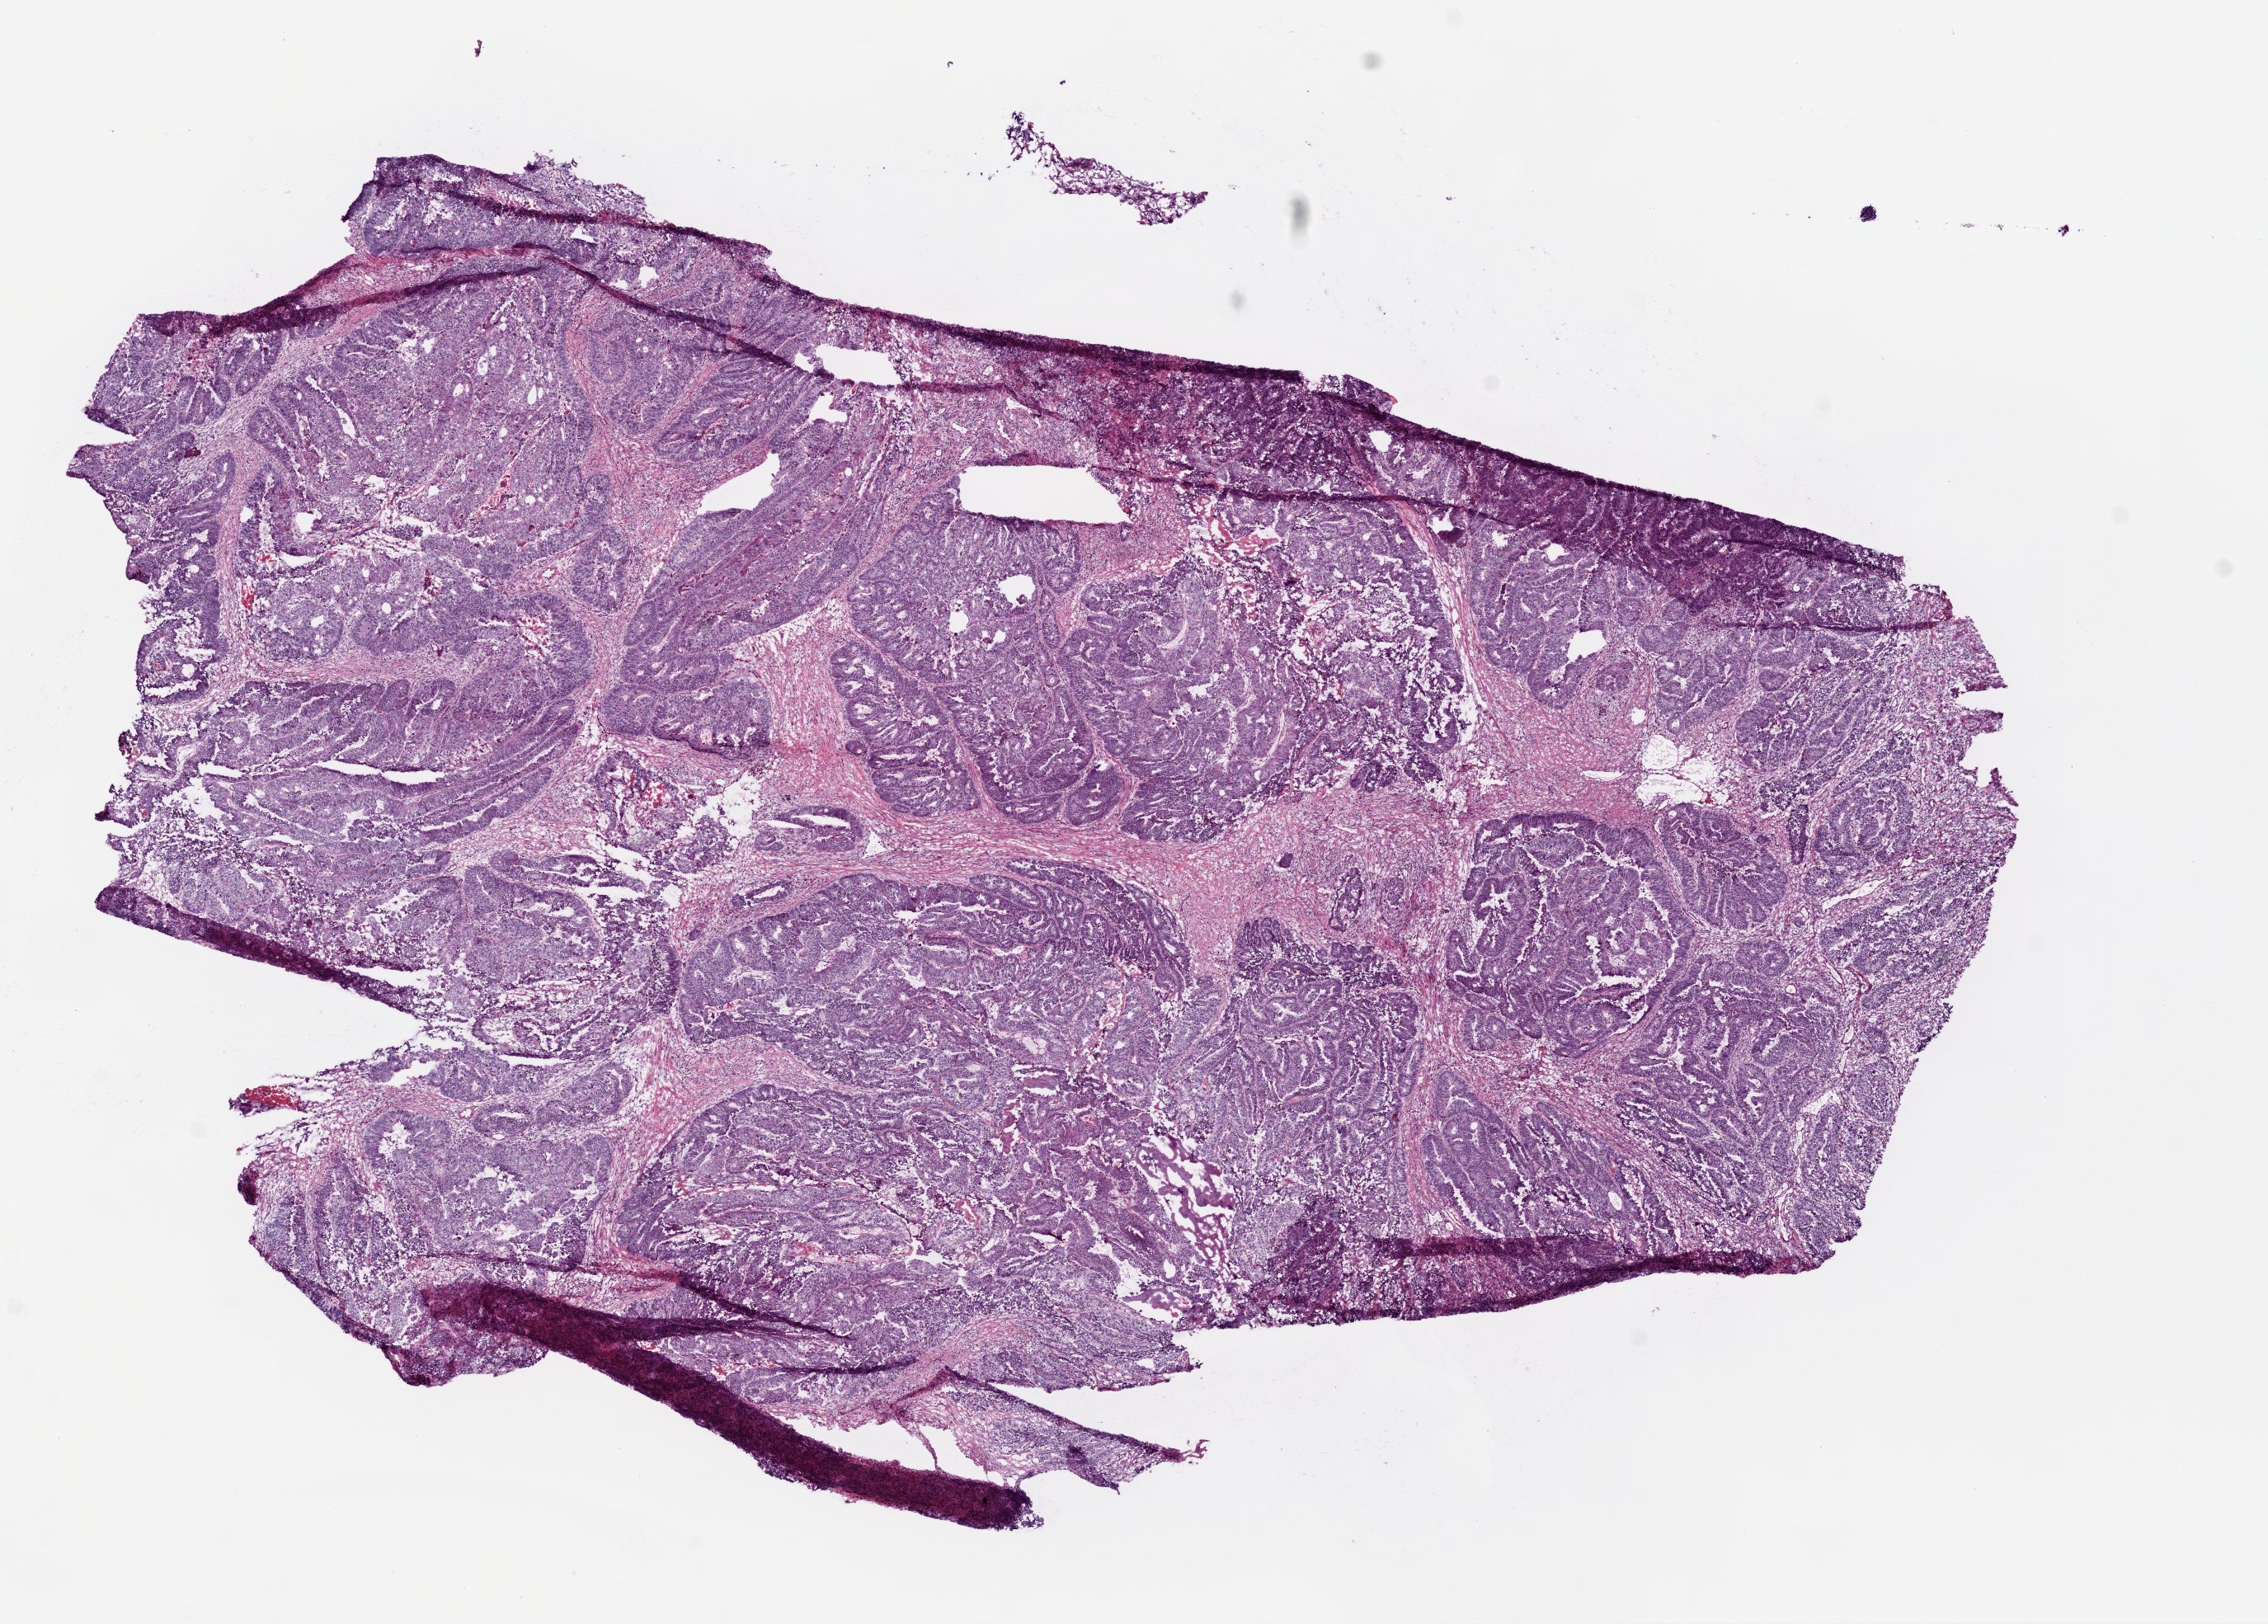
Digitized H&E tissue section (whole slide), a low-resolution overview of the entire scanned area, about 11.0 x 7.9 mm (acquisition: 20x scan). Frozen section. Sample: primary tumour, rectum. Female patient; age at initial diagnosis 85 years. Pathologist review of this section (percent, as recorded): tumour cells 75%, tumour nuclei 70%, normal cells 0%, stromal cells 15%, necrosis 10%.
Lymph nodes positive (case pathology): 0 of 18 examined. AJCC pathologic stage: I (5th edition). Diagnosis: Adenocarcinoma, NOS (colon, NOS).